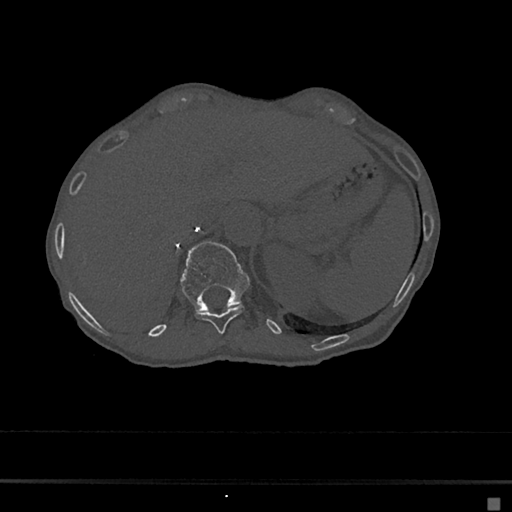
CT including the spine, one axial slice. Slice 149 of 797 in the series (ordered by position). Reconstruction kernel Br40s/3. Bone window (W 1800 / L 400 HU). 0.5 mm slice thickness. 512 × 512 image matrix, field of view 360 × 360 mm. Female patient, age 68 years. Case-level facts recorded for this patient, not image findings: primary cancer: renal.
Structures marked on this image (semi-automatic segmentation, software-assisted and operator-edited):
- T11 vertebra: bounding box (x1, y1, x2, y2) in pixels: (195, 304, 245, 334)
- T12 vertebra: (180, 242, 250, 311)